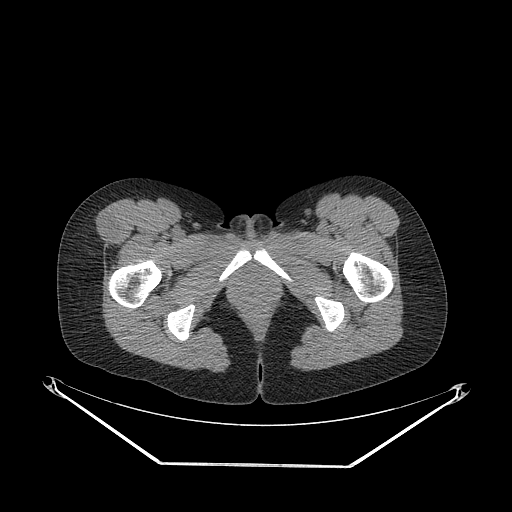
CT of an extremity soft-tissue mass (from a PET/CT study), one axial slice. Position 54 of 267 along the scan axis. Reconstruction kernel STANDARD. Soft-tissue window (W 400 / L 40 HU). 512 × 512 image matrix, field of view 500 × 500 mm. Female patient. Case-level facts recorded for this patient, not image findings: histological type: synovial sarcoma; grade: intermediate; site of the primary tumour: right thigh.
Structures marked on this image (expert contour drawn on MRI and transferred to this co-registered scan by the dataset authors):
- gross tumour volume including surrounding oedema: box from (x=91, y=215) to (x=117, y=245) px
- gross tumour volume (mass): (x=91, y=215)–(x=117, y=245)